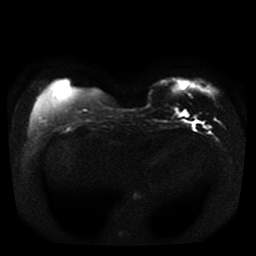
Breast MRI, one axial slice. Position 8 of 41 along the scan axis. Diffusion-weighted series; image 2 of 4 stored at this slice position (different b-values; order by instance number). 1.5 T. 5 mm slice thickness. 256 × 256 image matrix, field of view 330 × 330 mm. Female patient.
Annotated regions visible in this slice (manually delineated by an expert):
- tumour on diffusion-weighted imaging: box from (x=175, y=84) to (x=188, y=116) px